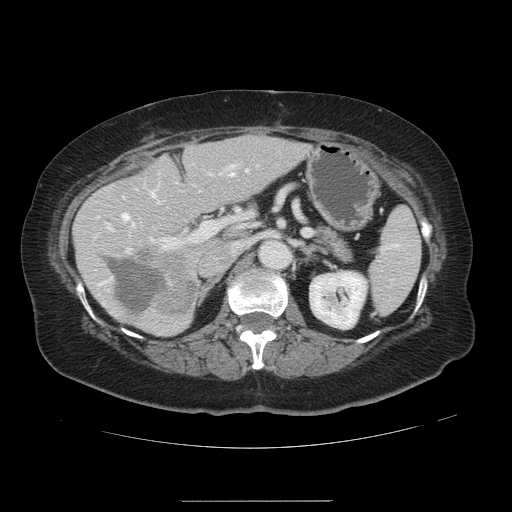
Contrast-enhanced abdominal CT, one axial slice; slice 71 of 141 in the series (ordered by position); intravenous contrast given; soft-tissue window (W 400 / L 40 HU); 2.5 mm slice thickness; 512 × 512 image matrix, field of view 393 × 393 mm. Female patient, age 74 years. From the clinical record (not read from this slice): diagnosis: colorectal cancer liver metastases, imaged before liver resection; multiple liver metastases: yes.
Annotated regions visible in this slice (manually delineated by an expert):
- hepatic veins: bounding box (x1, y1, x2, y2) in pixels: (122, 173, 233, 230)
- liver: (75, 136, 305, 335)
- planned liver remnant (the part of the liver to remain after resection): (76, 136, 305, 335)
- portal vein (with intrahepatic branches): (97, 164, 248, 253)
- liver metastasis: (109, 259, 166, 314)
- liver metastasis: (135, 248, 195, 315)